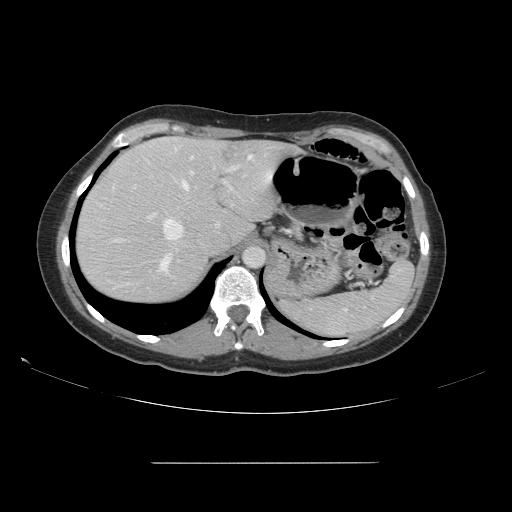
Contrast-enhanced abdominal CT, one axial slice. Position 117 of 151 along the scan axis. Intravenous contrast given. Soft-tissue window (W 400 / L 40 HU). 2.5 mm slice thickness. 512 × 512 image matrix, field of view 421 × 421 mm. Female patient, age 46 years. From the clinical record (not read from this slice): diagnosis: colorectal cancer liver metastases, imaged before liver resection.
Annotated regions visible in this slice (manually delineated by an expert):
- hepatic veins: box from (x=115, y=154) to (x=254, y=241) px
- liver: (x=76, y=137)–(x=298, y=305)
- planned liver remnant (the part of the liver to remain after resection): (x=89, y=137)–(x=294, y=251)
- portal vein (with intrahepatic branches): (x=133, y=166)–(x=236, y=272)
- liver metastasis: (x=222, y=145)–(x=239, y=163)